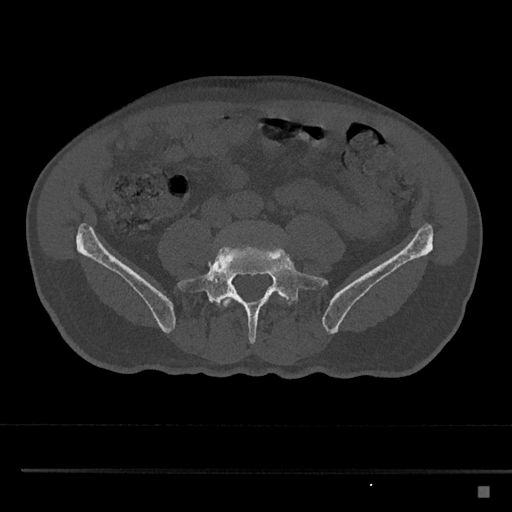
CT including the spine, one axial slice; slice 594 of 797 in the series (ordered by position); 120 kVp; bone window (W 1800 / L 400 HU); 512 × 512 image matrix, field of view 391 × 391 mm. Patient: male, 59 years. Case-level facts recorded for this patient, not image findings: primary cancer: prostate.
Structures marked on this image (semi-automatically segmented with operator editing):
- L4 vertebra: bounding box <217,227,241,307> (left, top, right, bottom; pixels)
- L5 vertebra: <177,239,328,344>